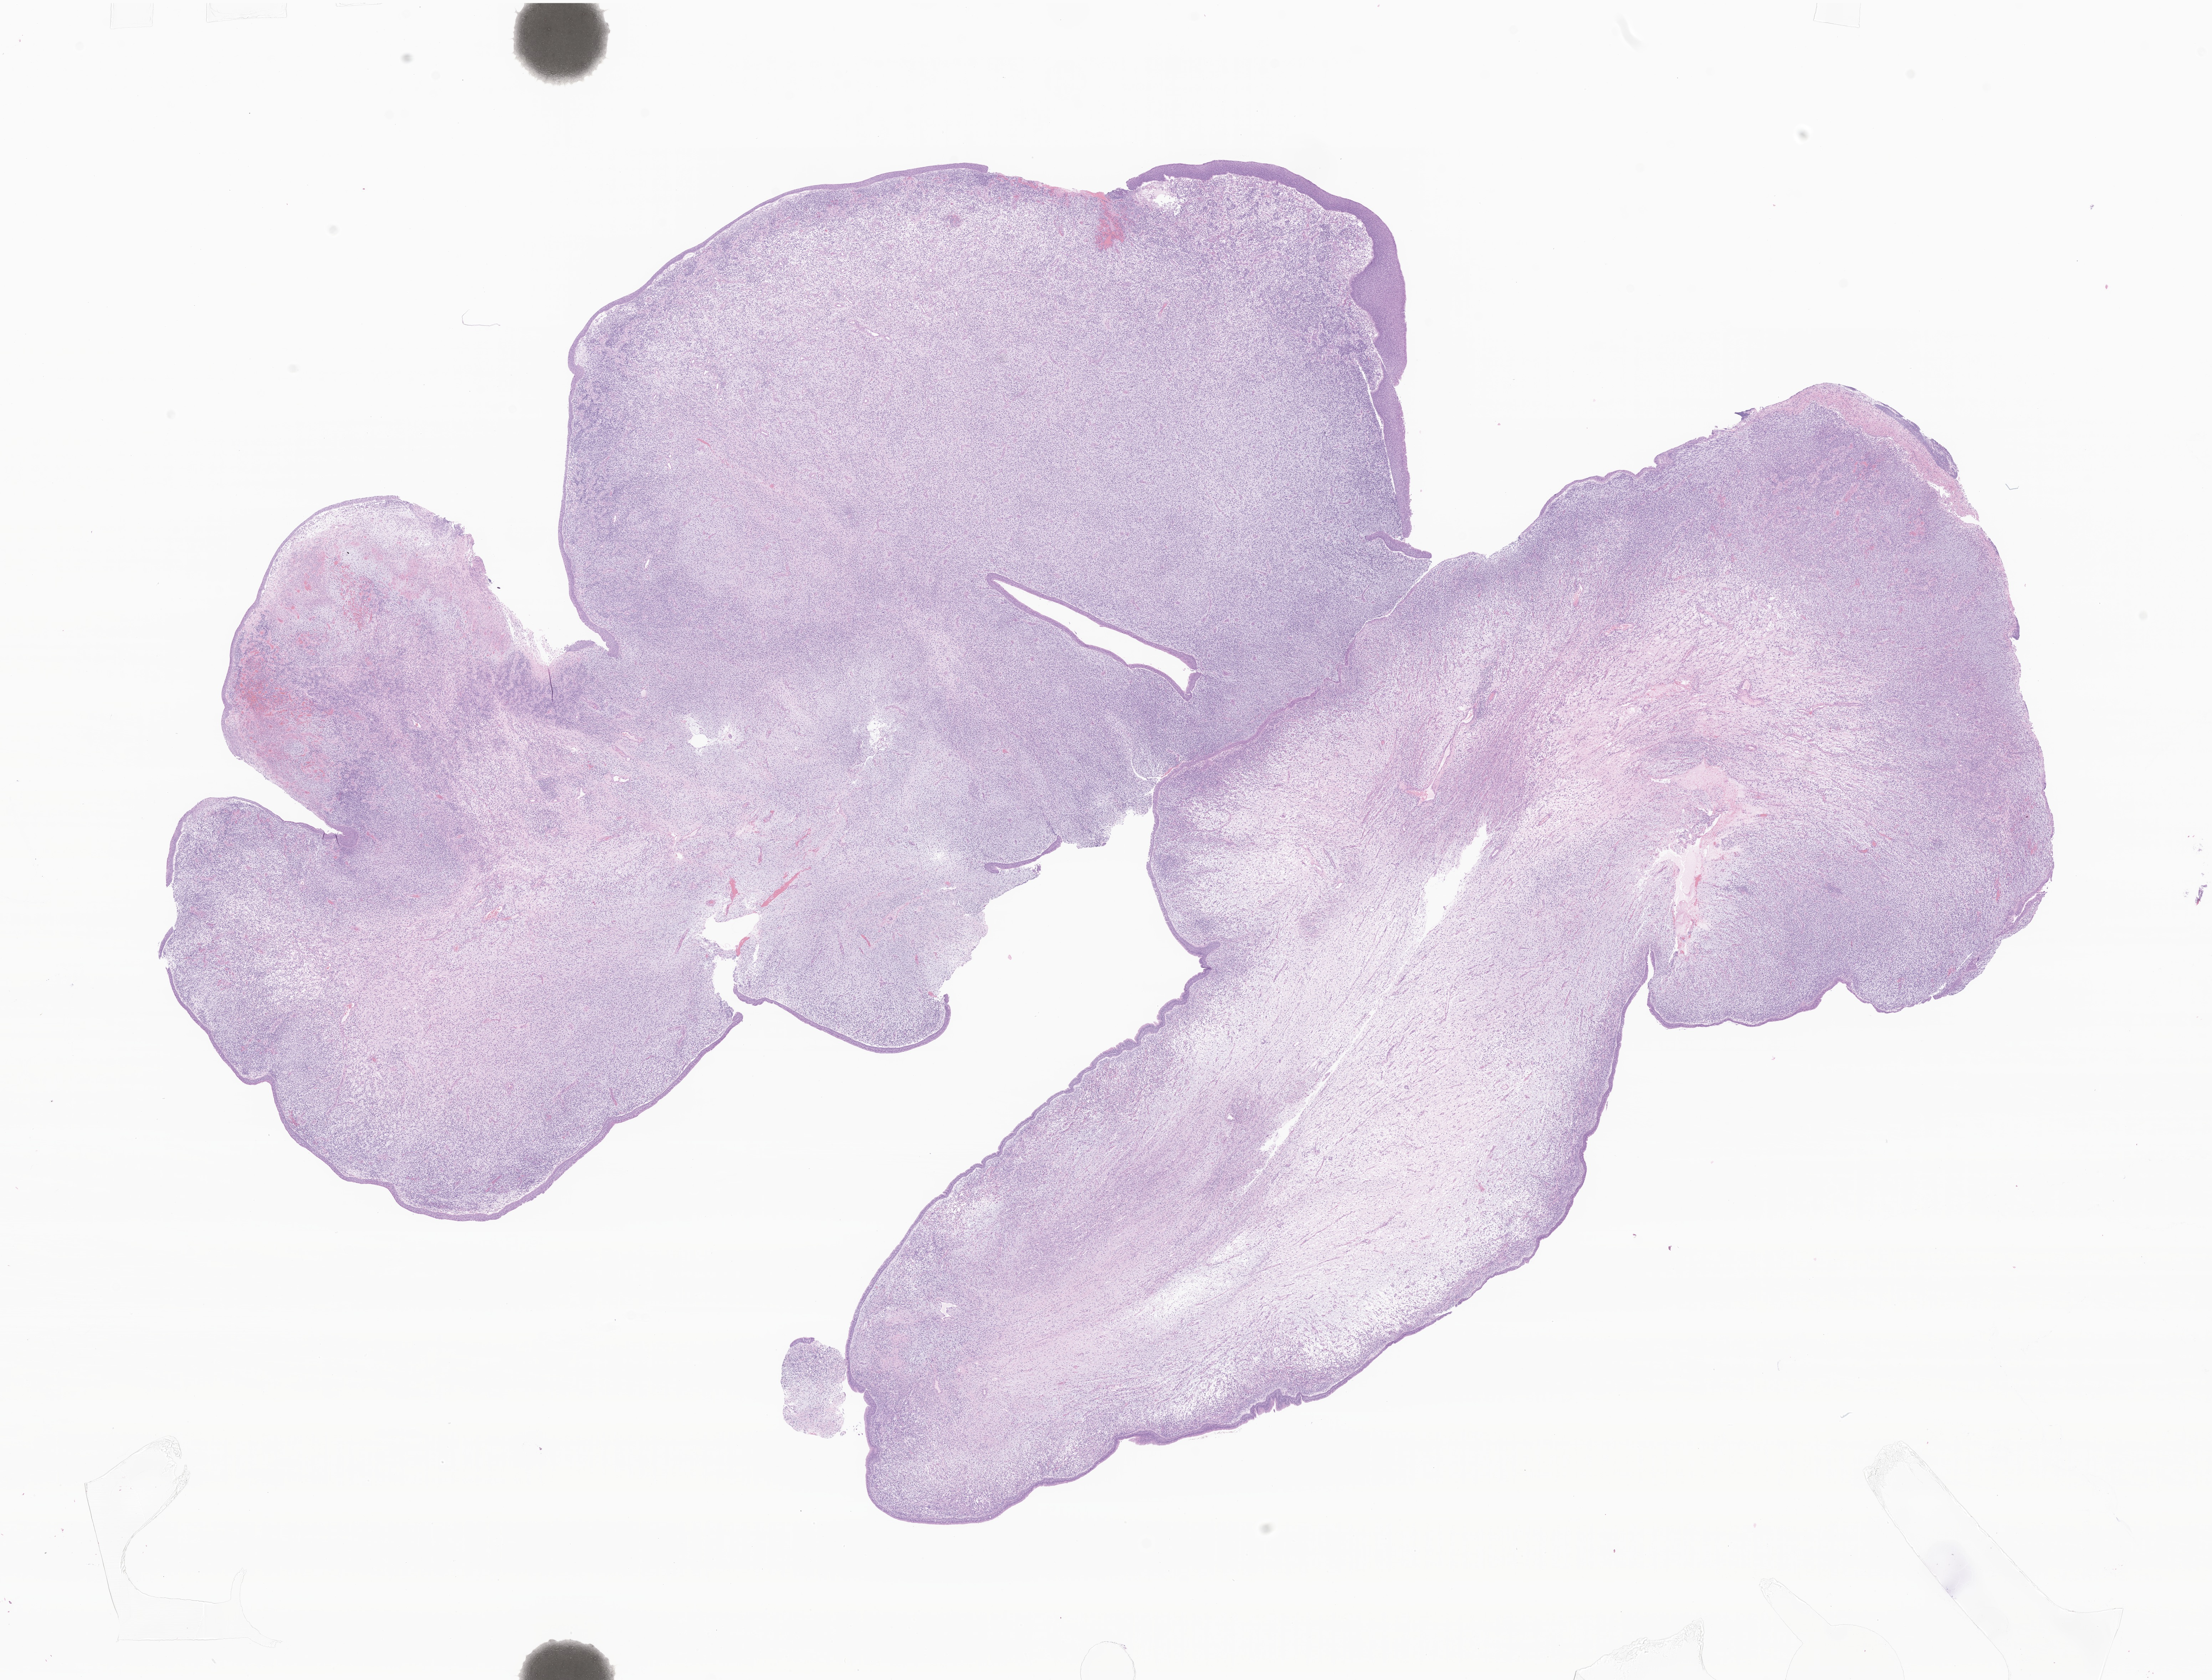
Whole-slide image, H&E stain of tumor tissue from the nasal cavity — whole scanned area (about 26.2 x 19.9 mm) shown as a low-resolution overview. Formalin-fixed, paraffin-embedded (FFPE) tissue. Patient male; age 736 days (about 2.0 years).
Recorded diagnosis: Rhabdomyosarcoma, NOS.